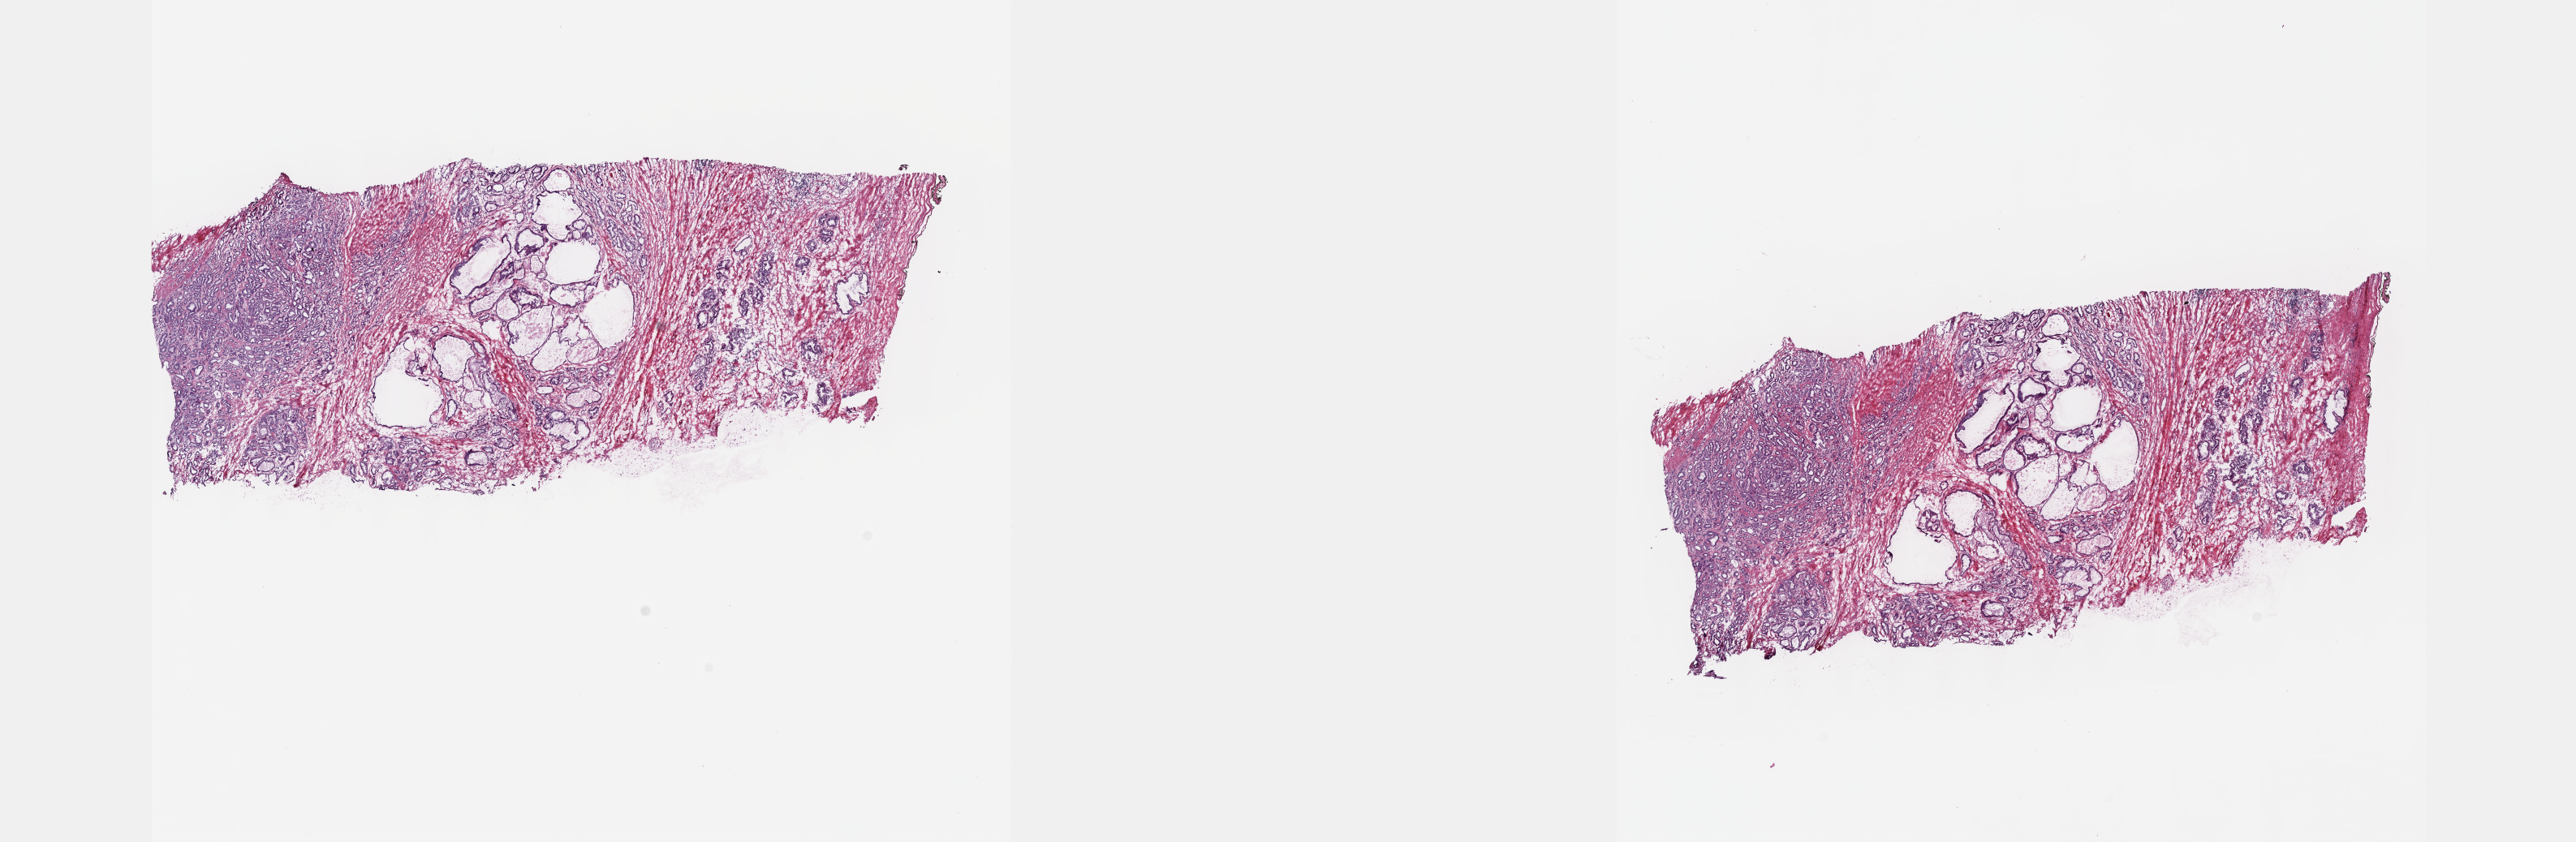
Hematoxylin and eosin (H&E) stained whole-slide image — whole scanned area (about 25.7 x 8.4 mm, slide scanned at 40x) shown as a low-resolution overview. Frozen section from the top of the tissue portion. Sample: primary tumour, prostate. Male patient; age at initial diagnosis 59 years. Gleason score: 6 (3+3). Slide review estimates, as recorded: tumour cells 45%, tumour nuclei 60%, normal cells 25%, stromal cells 30%, necrosis 0%. Infiltration values recorded for this section: lymphocyte infiltration 0%, monocyte infiltration 0%, neutrophil infiltration 0%.
Histologic diagnosis: Adenocarcinoma, NOS (prostate gland). Lymph nodes positive (case pathology): 0 of 12 examined. Laterality: bilateral.